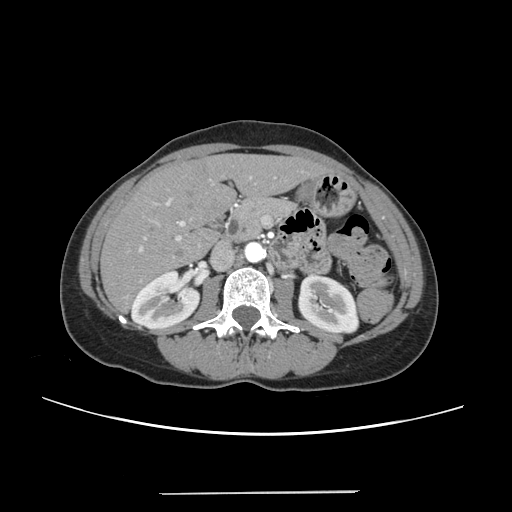
Contrast-enhanced abdominal CT, one axial slice. 120 kVp. Intravenous contrast given. Soft-tissue window (W 400 / L 40 HU). 1.25 mm slice thickness. 512 × 512 image matrix, field of view 371 × 371 mm. Female patient, age 60 years. Case-level facts recorded for this patient, not image findings: diagnosis: colorectal cancer liver metastases, imaged before liver resection; multiple liver metastases: no; largest metastasis: 1.5 cm; disease in both lobes: no.
Structures marked on this image (expert manual segmentation):
- liver: bounding box [x1, y1, x2, y2] px = [102, 155, 324, 310]
- planned liver remnant (the part of the liver to remain after resection): [102, 156, 324, 310]
- portal vein (with intrahepatic branches): [138, 176, 252, 253]